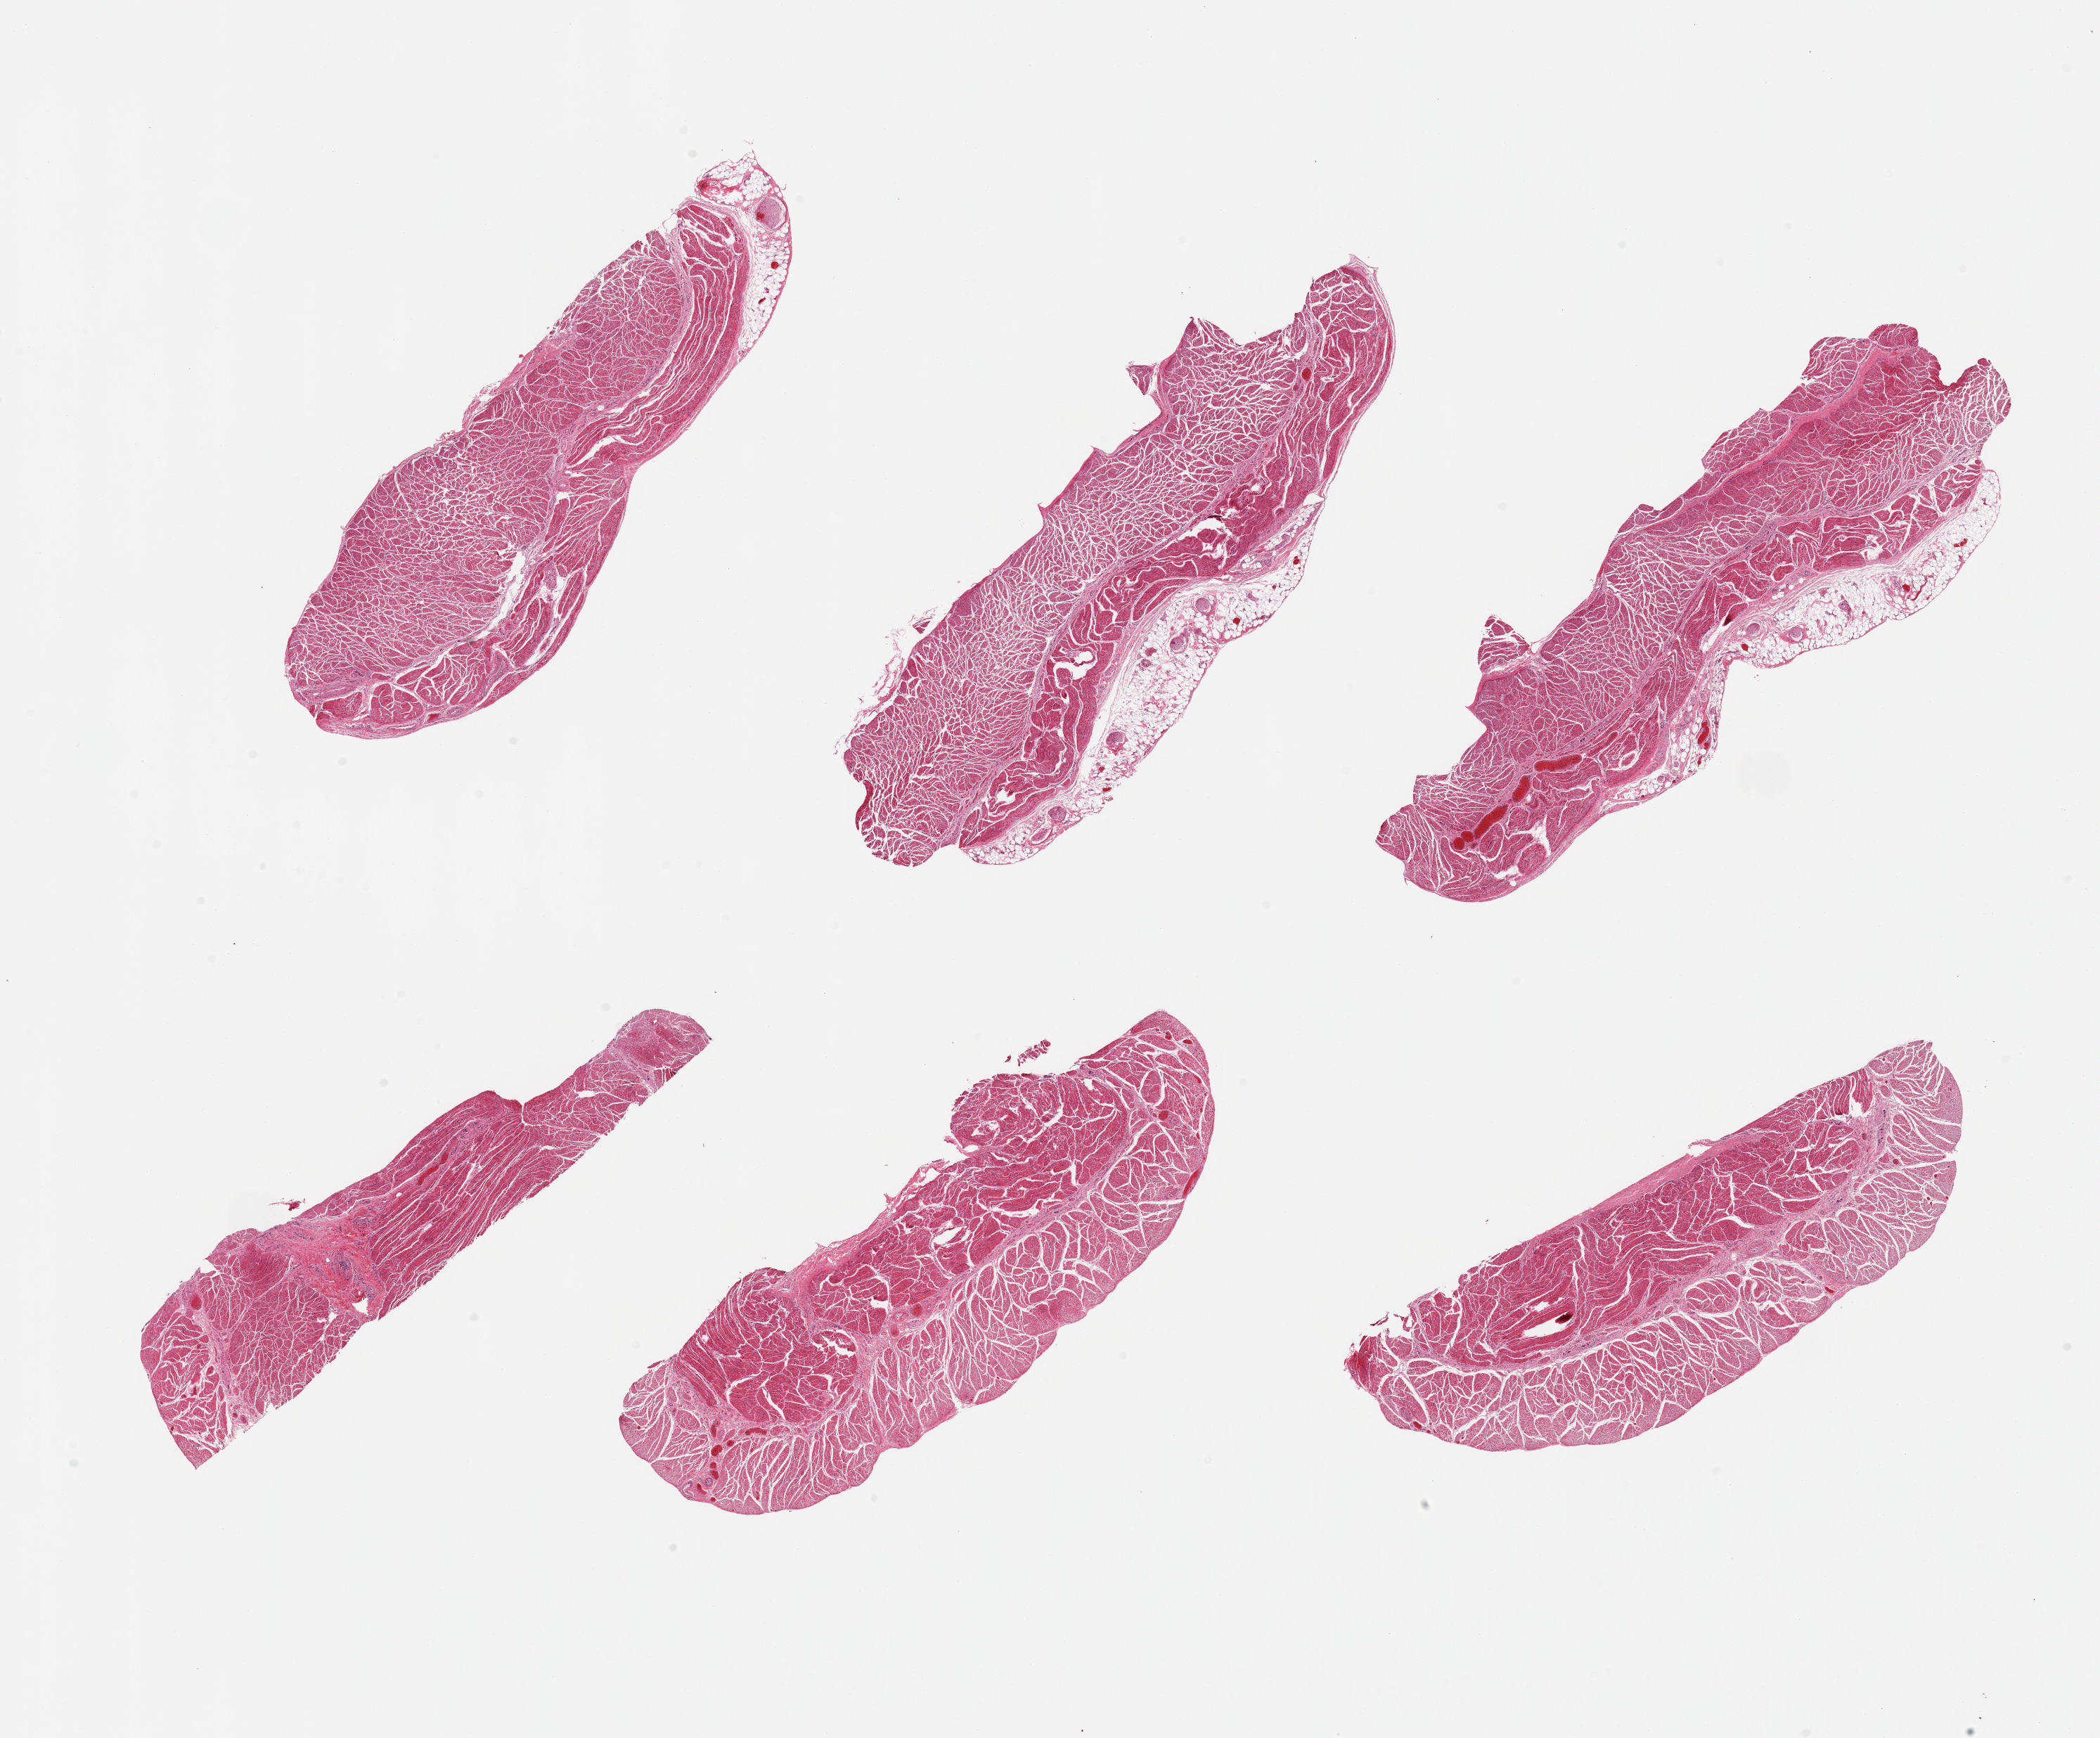
Whole-slide image, H&E stain — a low-resolution overview of the entire scanned area, about 23.6 x 19.6 mm (acquisition: 20x scan), PAXgene-fixed paraffin-embedded (PFPE) section, sampled site (target tissue): esophageal muscle, donor tissue sample. Male donor.
Pathologist's review note for this sample: 6 pieces, all target muscularis, a few with up to ~1mm ahderent fat.